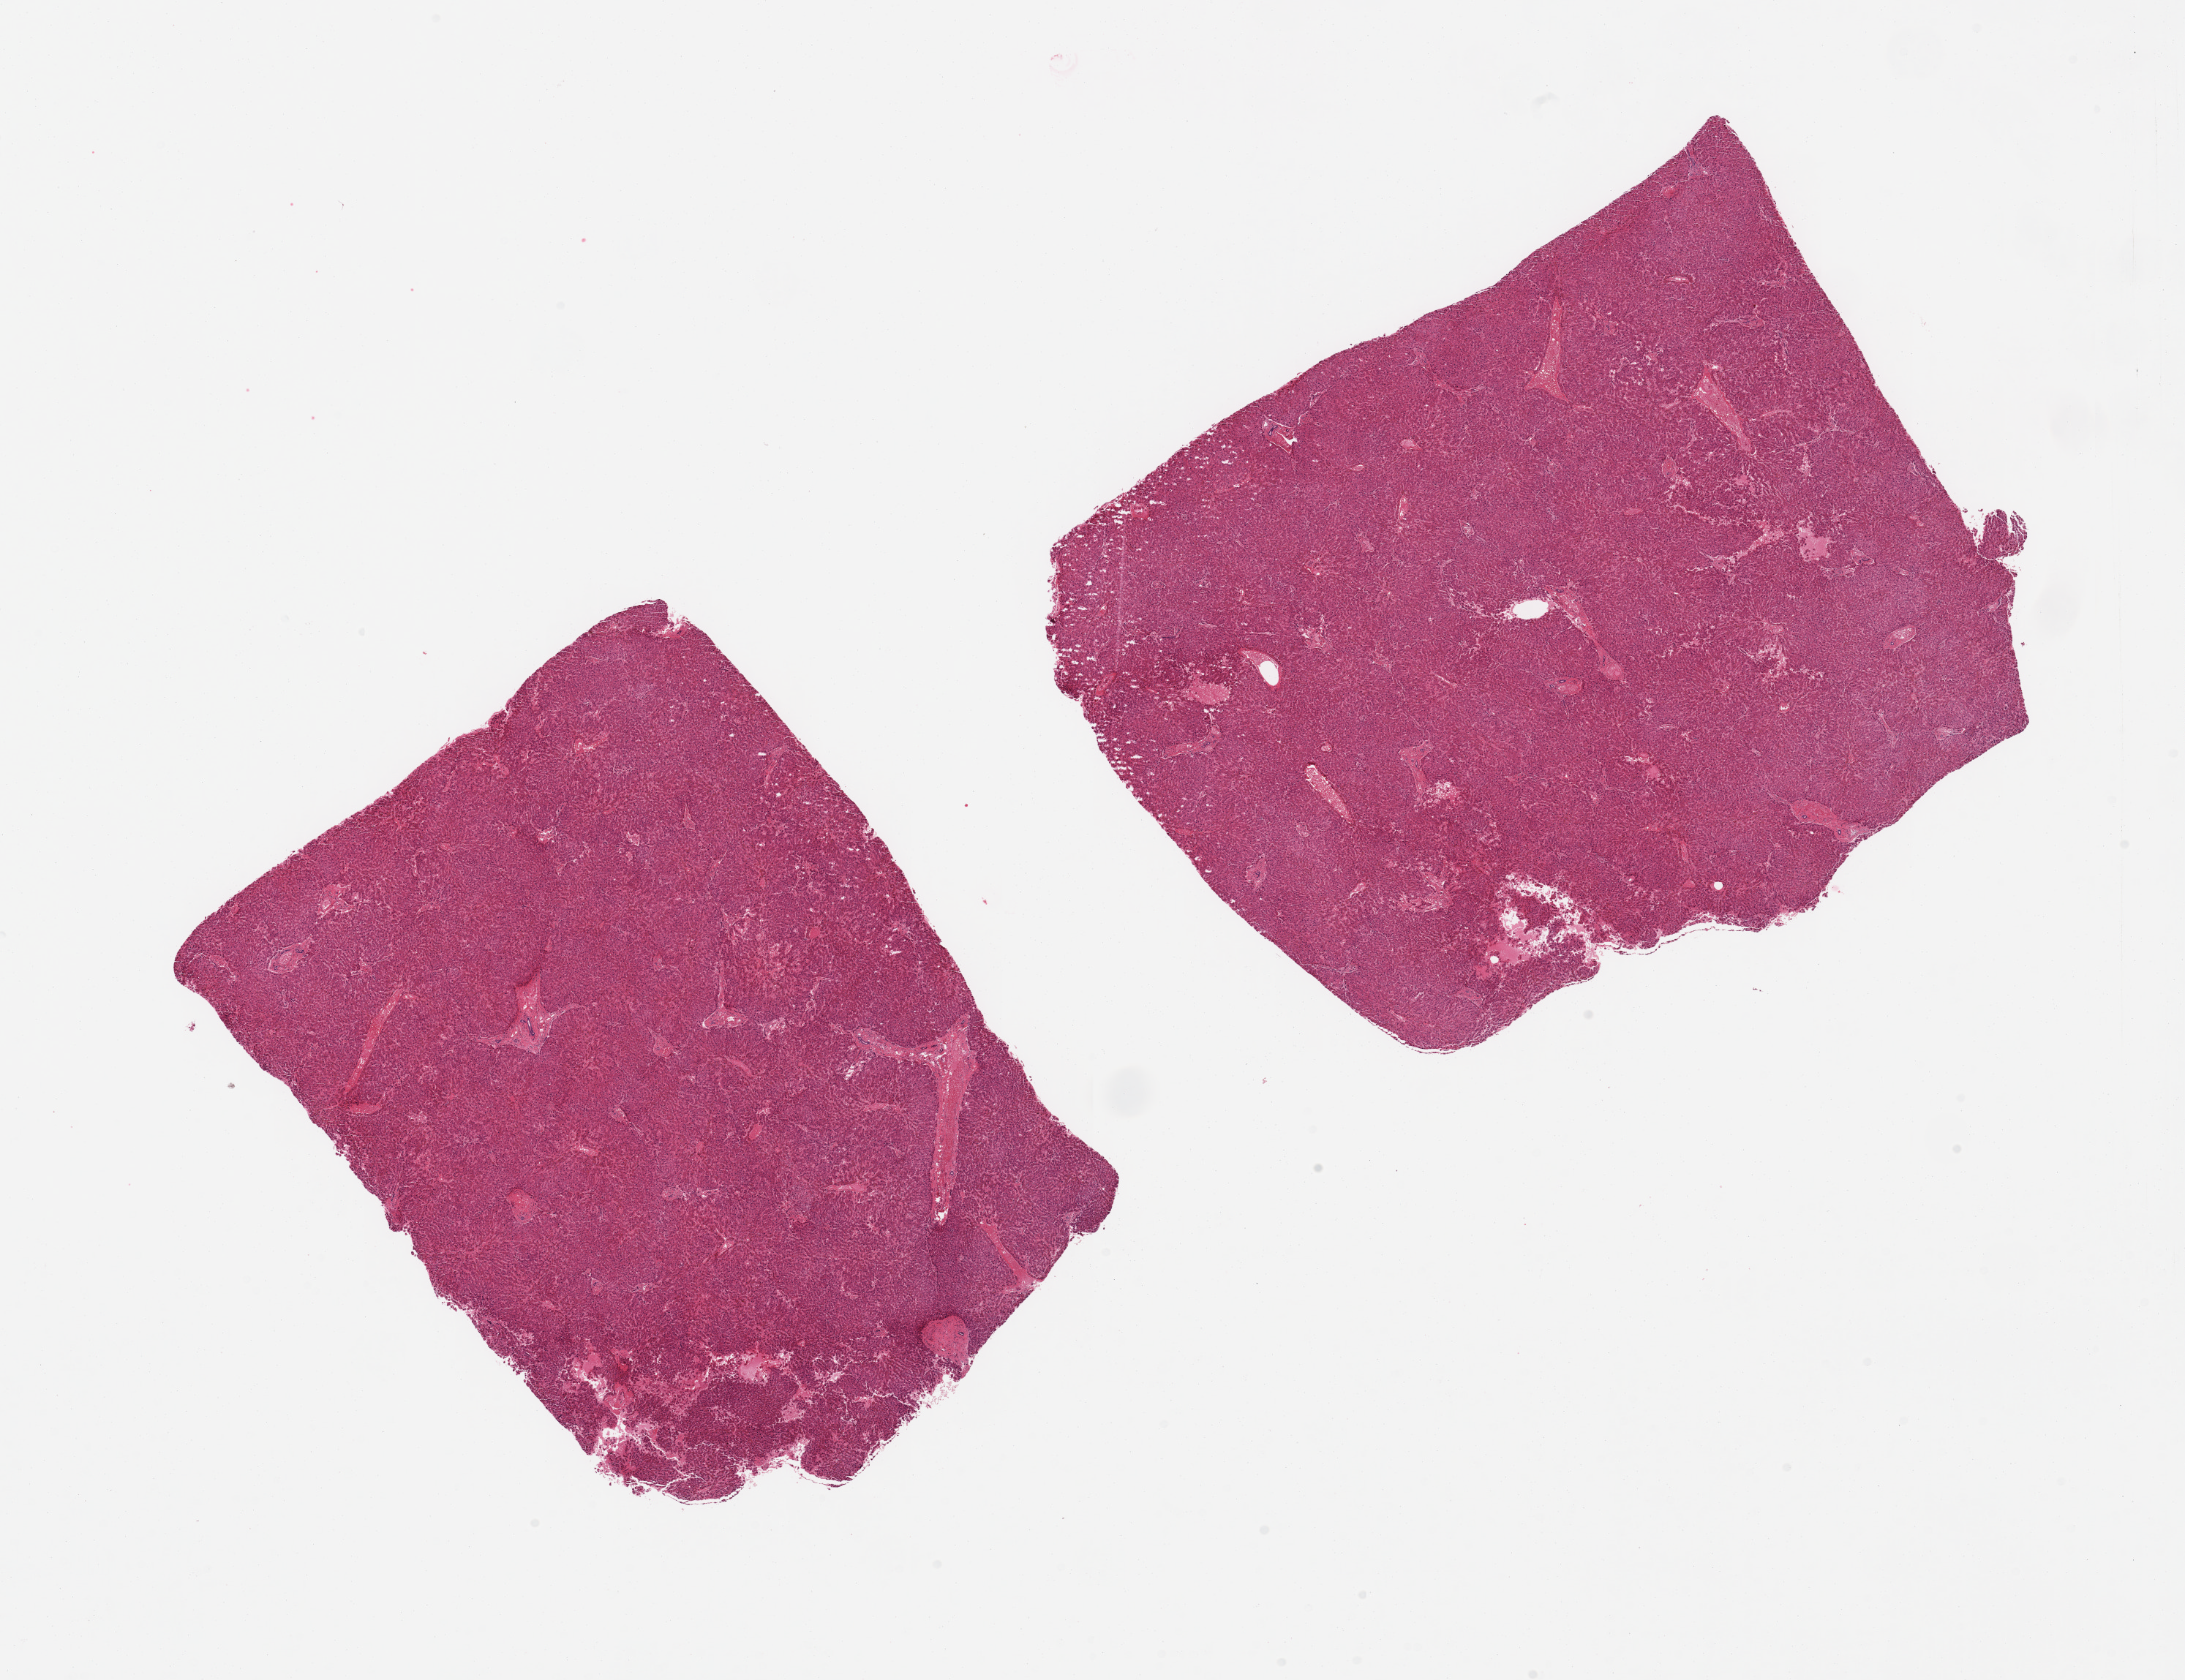
Haematoxylin and eosin whole-slide image, brightfield, whole scanned area (about 23.6 x 18.2 mm) shown as a low-resolution overview. PAXgene-fixed paraffin-embedded (PFPE) section. Section of liver (target tissue). Tissue donor sample. Female donor.
Reviewer comment on this tissue sample: 2 pieces, minimal steatosis.